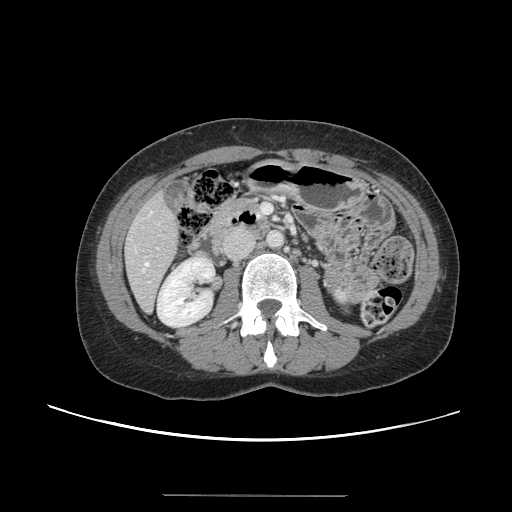
Contrast-enhanced abdominal CT, one axial slice. Slice 45 of 144 in the series (ordered by position). 120 kVp. Soft-tissue window (W 400 / L 40 HU). 2.5 mm slice thickness. 512 × 512 image matrix, field of view 380 × 380 mm. Female patient, age 53 years. Case-level facts recorded for this patient, not image findings: diagnosis: colorectal cancer liver metastases, imaged before liver resection; multiple liver metastases: yes; largest metastasis: 1.1 cm.
Structures marked on this image (expert manual segmentation):
- hepatic veins: bounding box [x1, y1, x2, y2] px = [143, 262, 149, 271]
- liver: [125, 195, 180, 311]
- planned liver remnant (the part of the liver to remain after resection): [126, 195, 180, 311]
- portal vein (with intrahepatic branches): [148, 248, 159, 283]